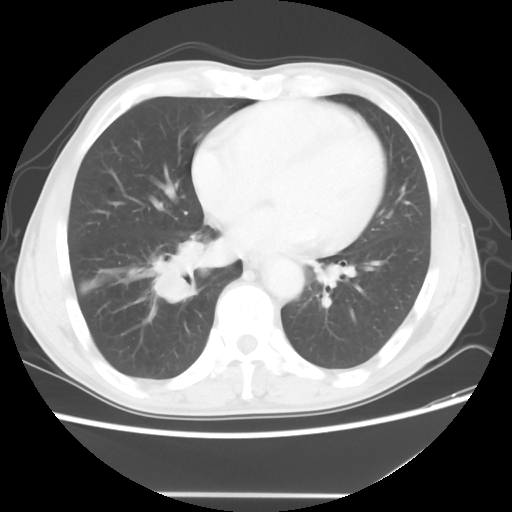
Chest CT, one axial slice. Slice 21 of 56 in the series (ordered by position). Reconstruction kernel STANDARD. 120 kVp. Lung window (W 1500 / L -600 HU). 5 mm slice thickness. 512 × 512 image matrix, field of view 344 × 344 mm. Patient: male, 65 years. Case-level facts recorded for this patient, not image findings: clinical TNM (as recorded): T1c N3 M0; histopathological grade: G3.
Structures marked on this image (bounding box drawn by a radiologist):
- lung tumour (recorded histology: small cell carcinoma): bounding box [x1, y1, x2, y2] px = [151, 231, 214, 306]